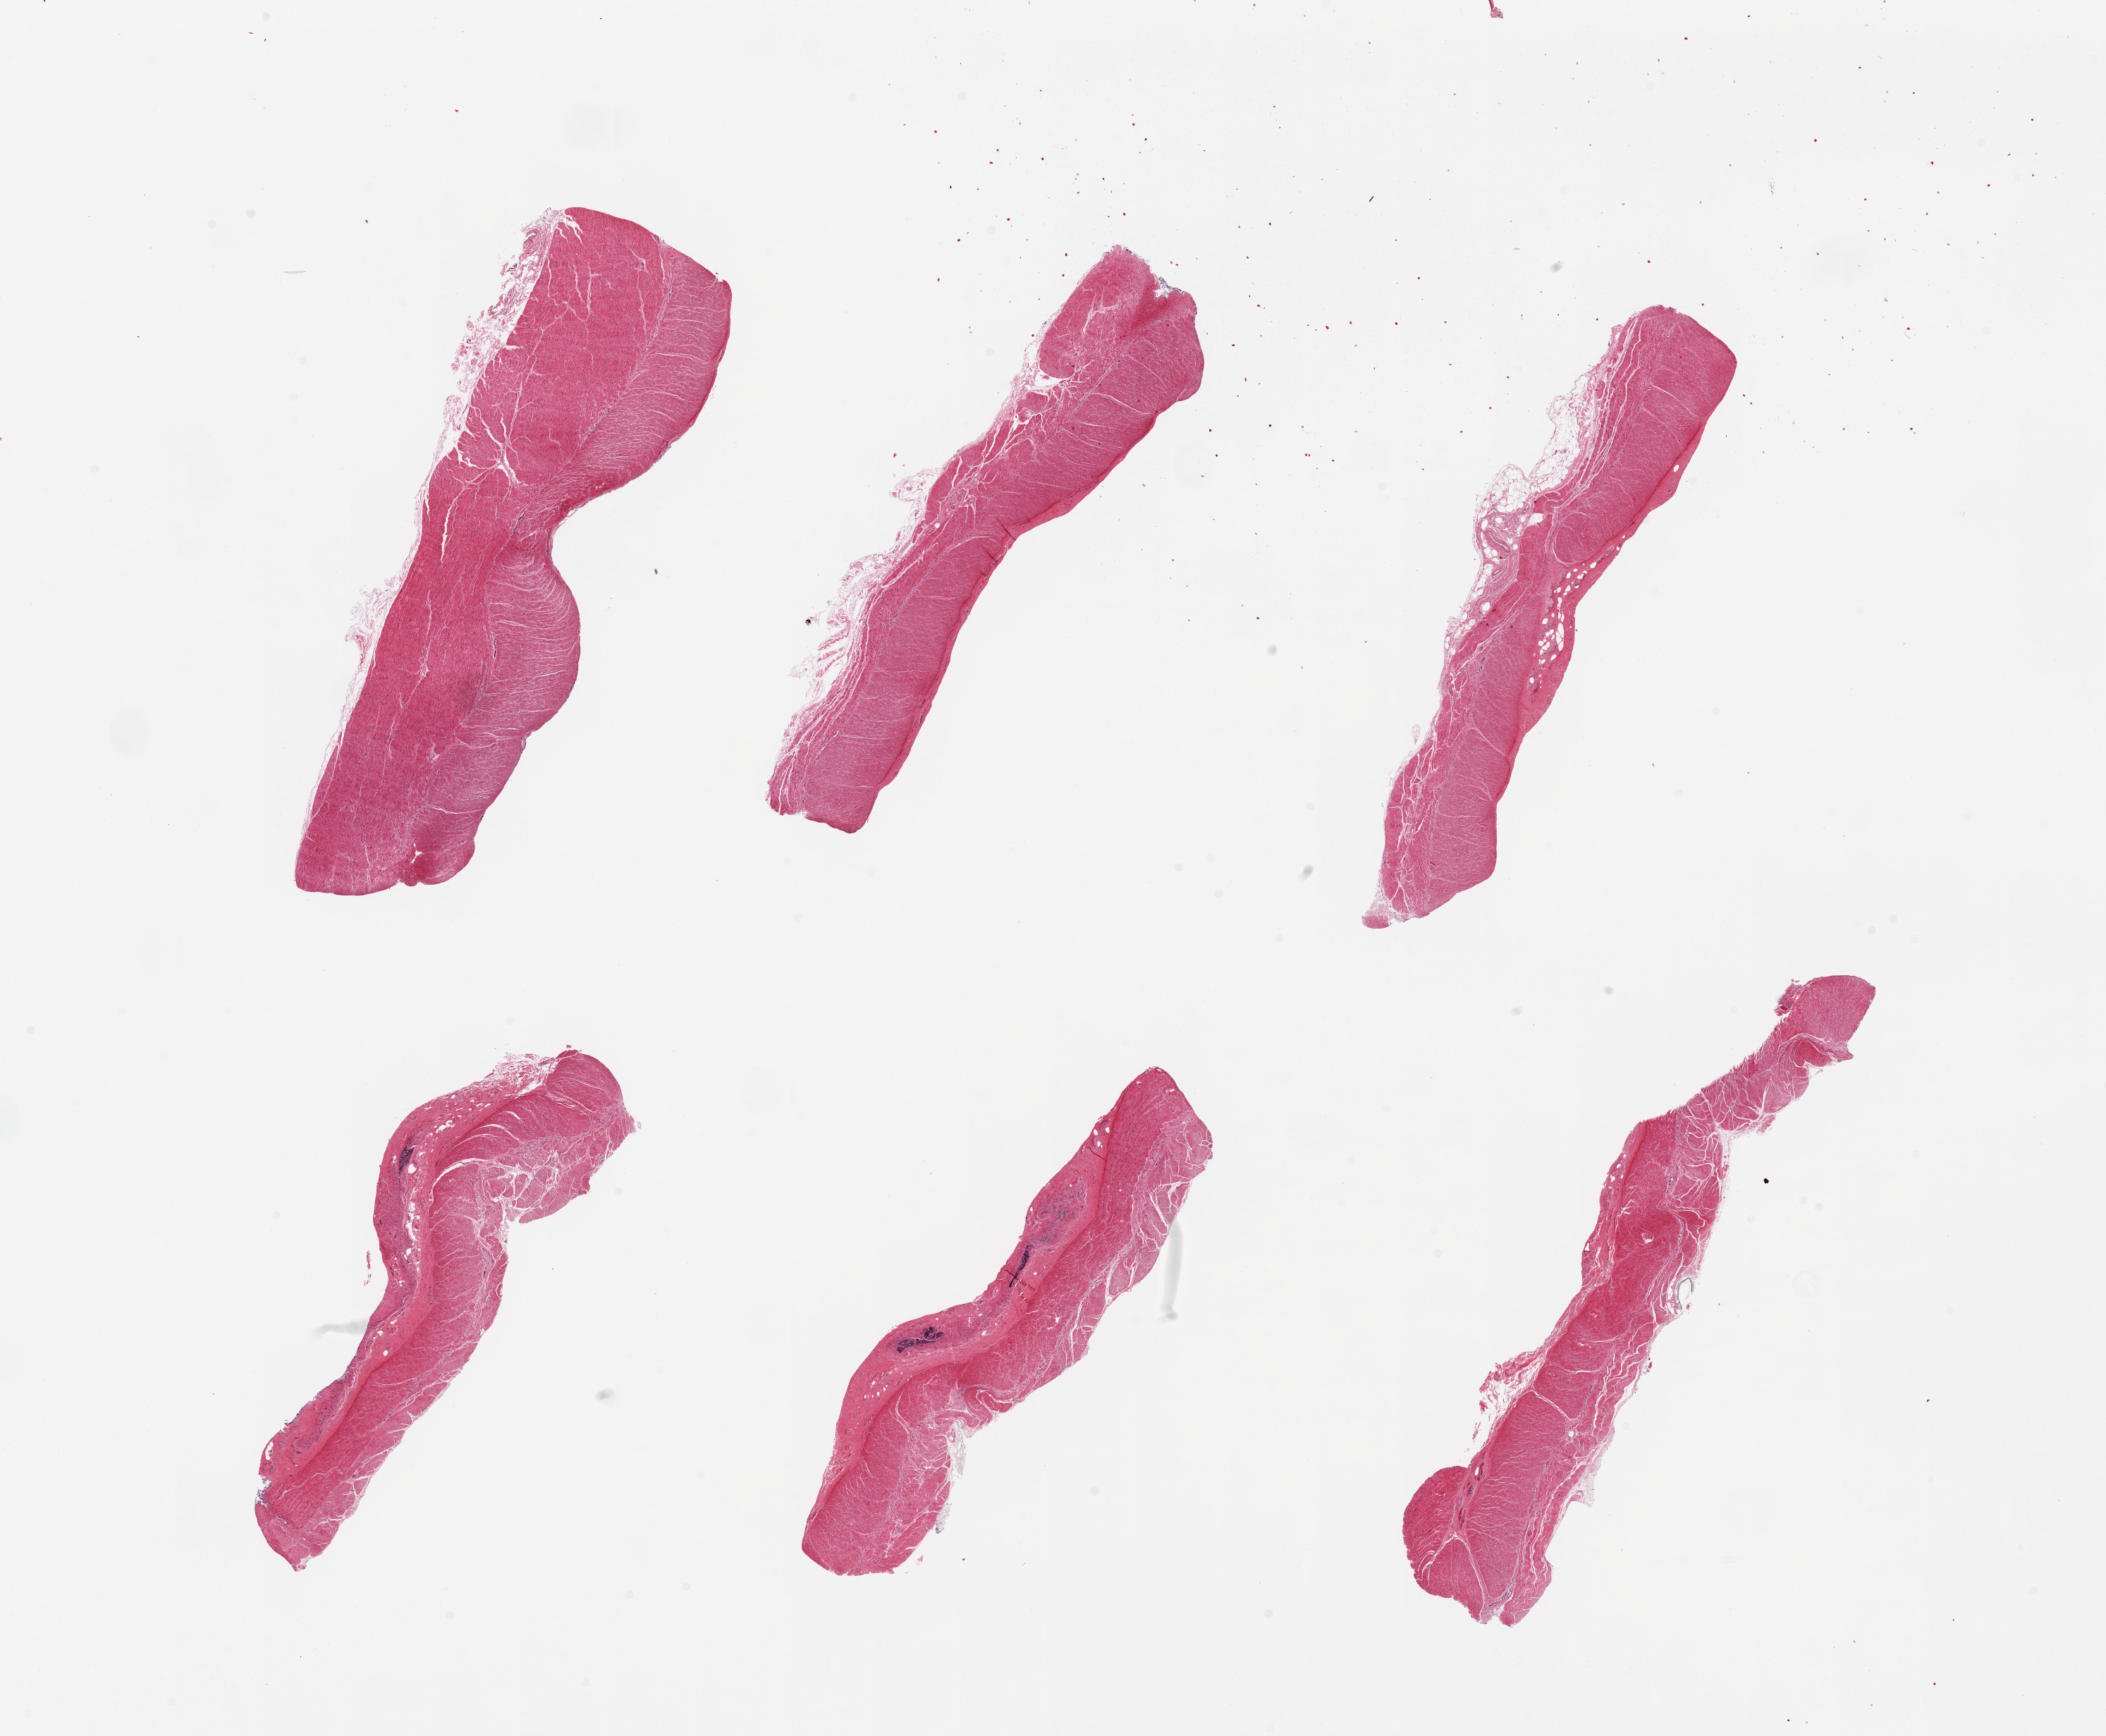
Digitized H&E-stained section, brightfield, a low-resolution overview of the entire scanned area, about 23.6 x 19.5 mm (acquisition: 20x scan); PAXgene-fixed paraffin-embedded (PFPE) section; target tissue: sigmoid colon; donor tissue sample. Donor: female.
Review note (as recorded): 6 pieces; confirmed target muscularis, few small lymphoid aggregates.